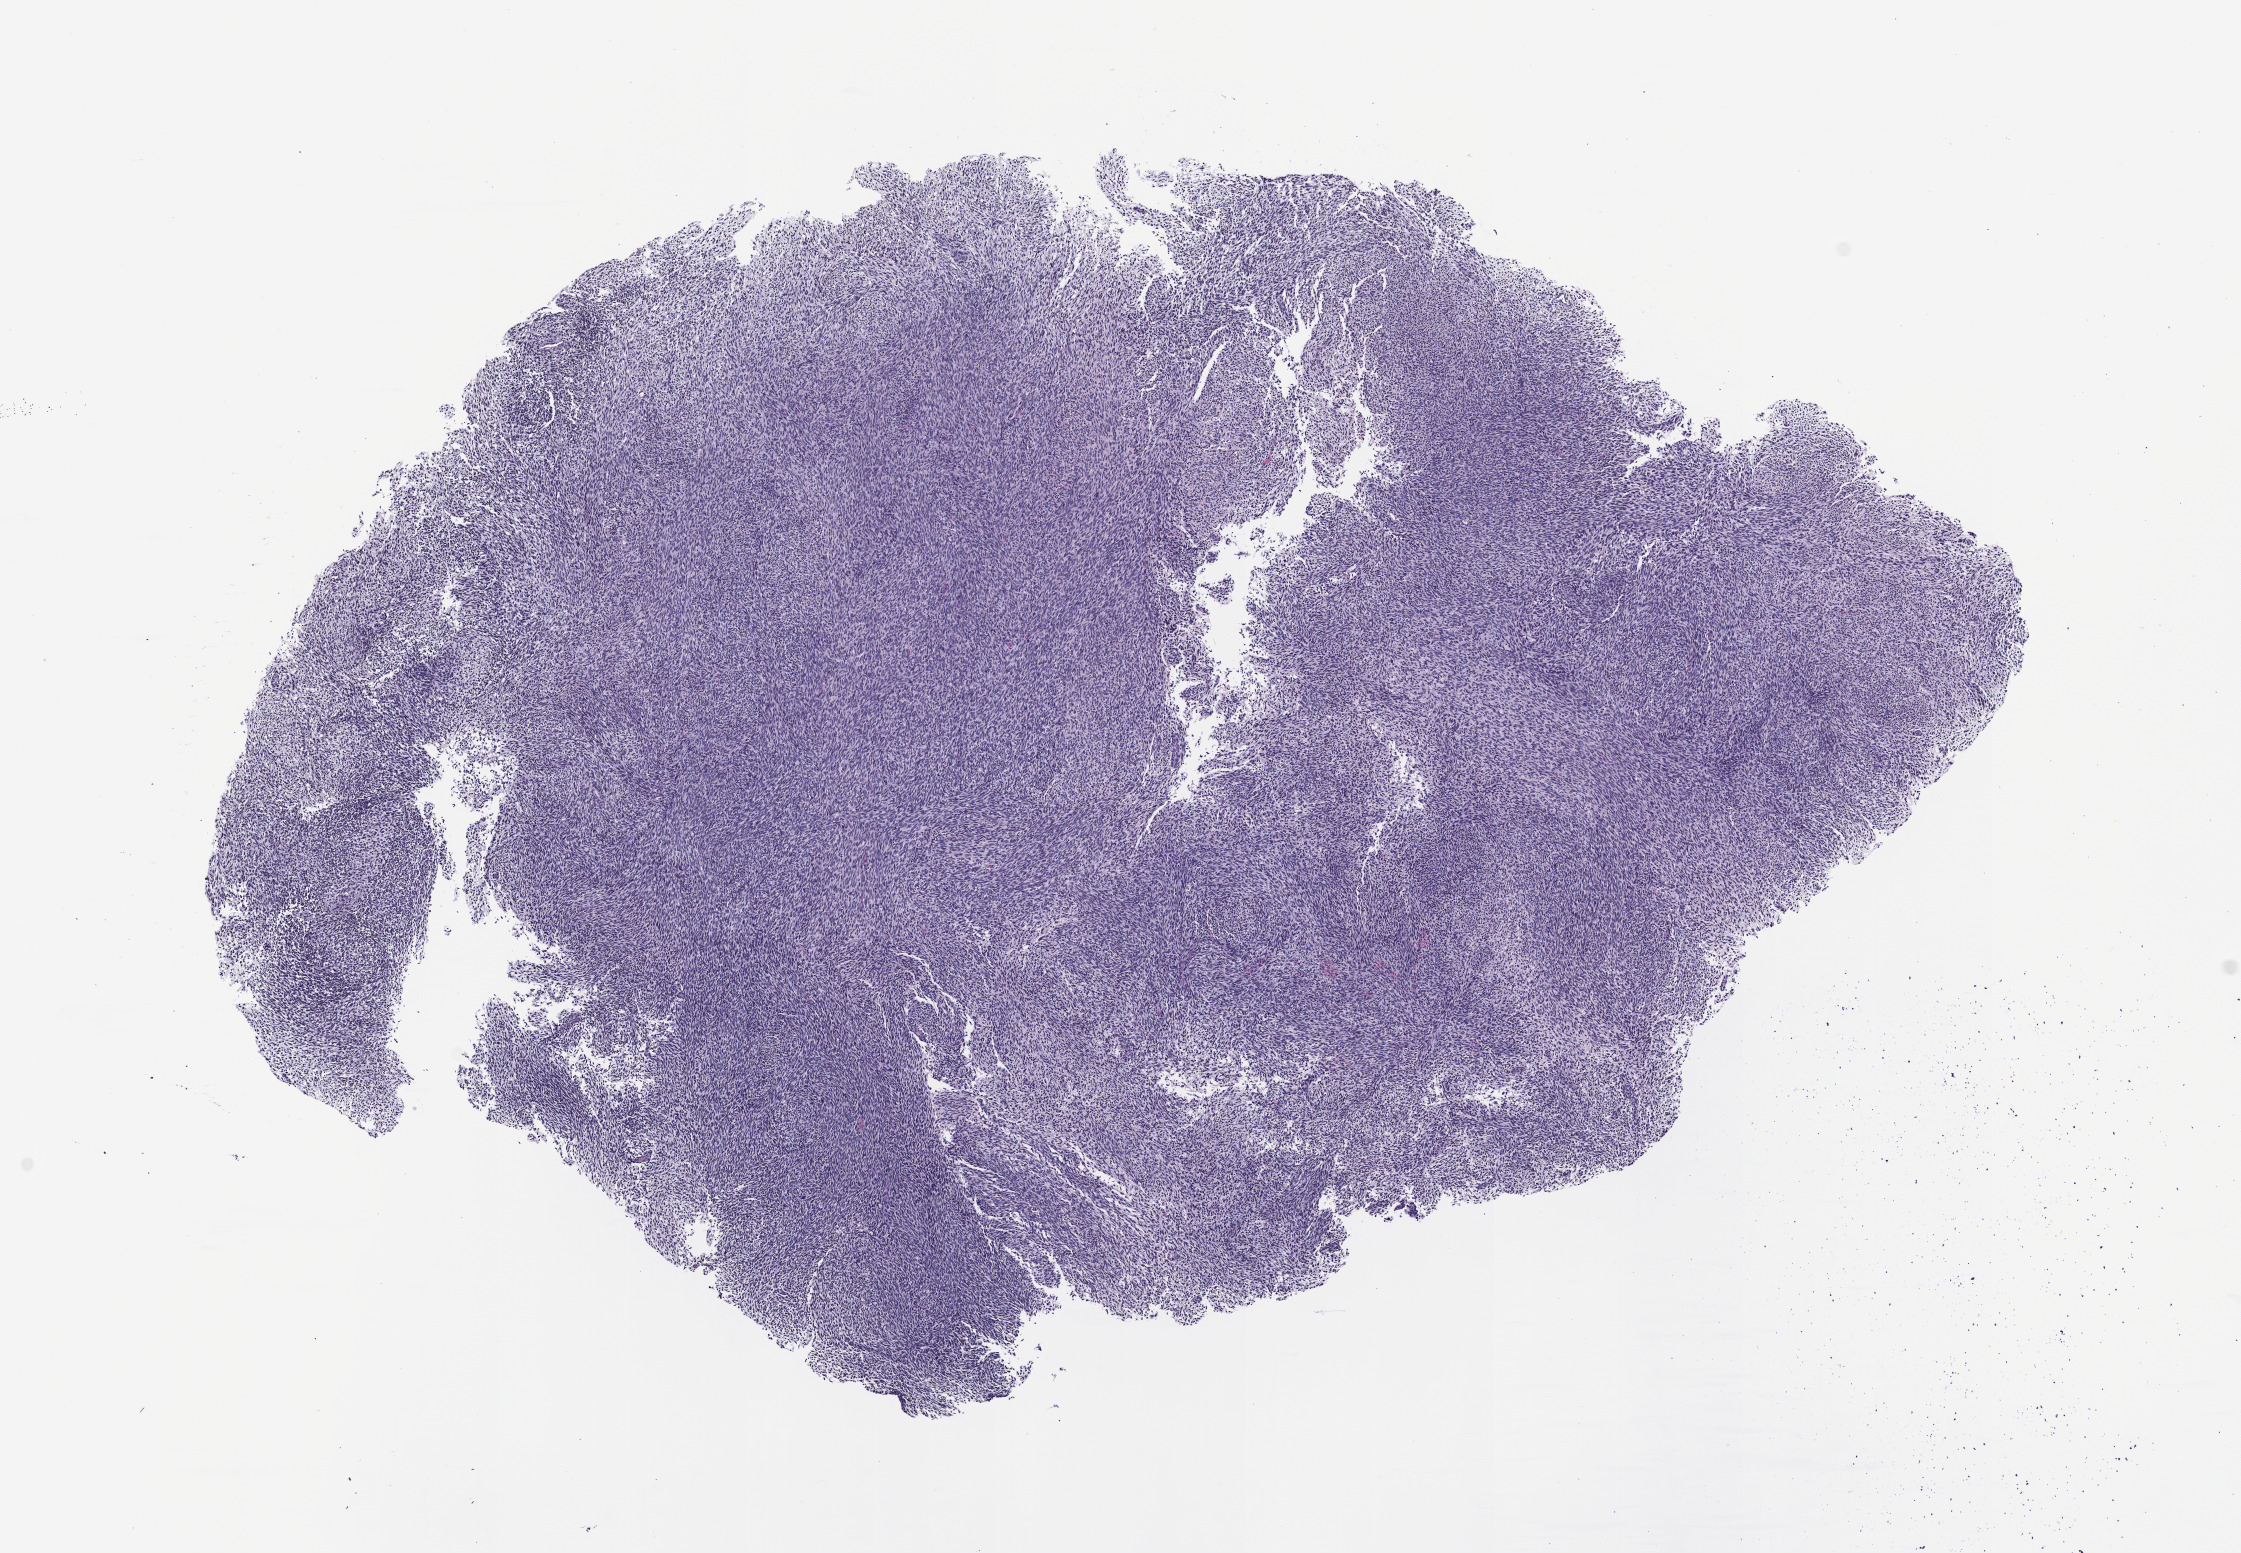
H&E whole-slide image of the patient's (originator) tumor tissue — a low-resolution overview of the entire scanned area, about 9.0 x 6.2 mm, formalin-fixed paraffin-embedded section, originating tumor site category: peripheral nervous system. Patient female; aged 37.
Diagnosis: Malignant Peripheral Nerve Sheath Tumor.